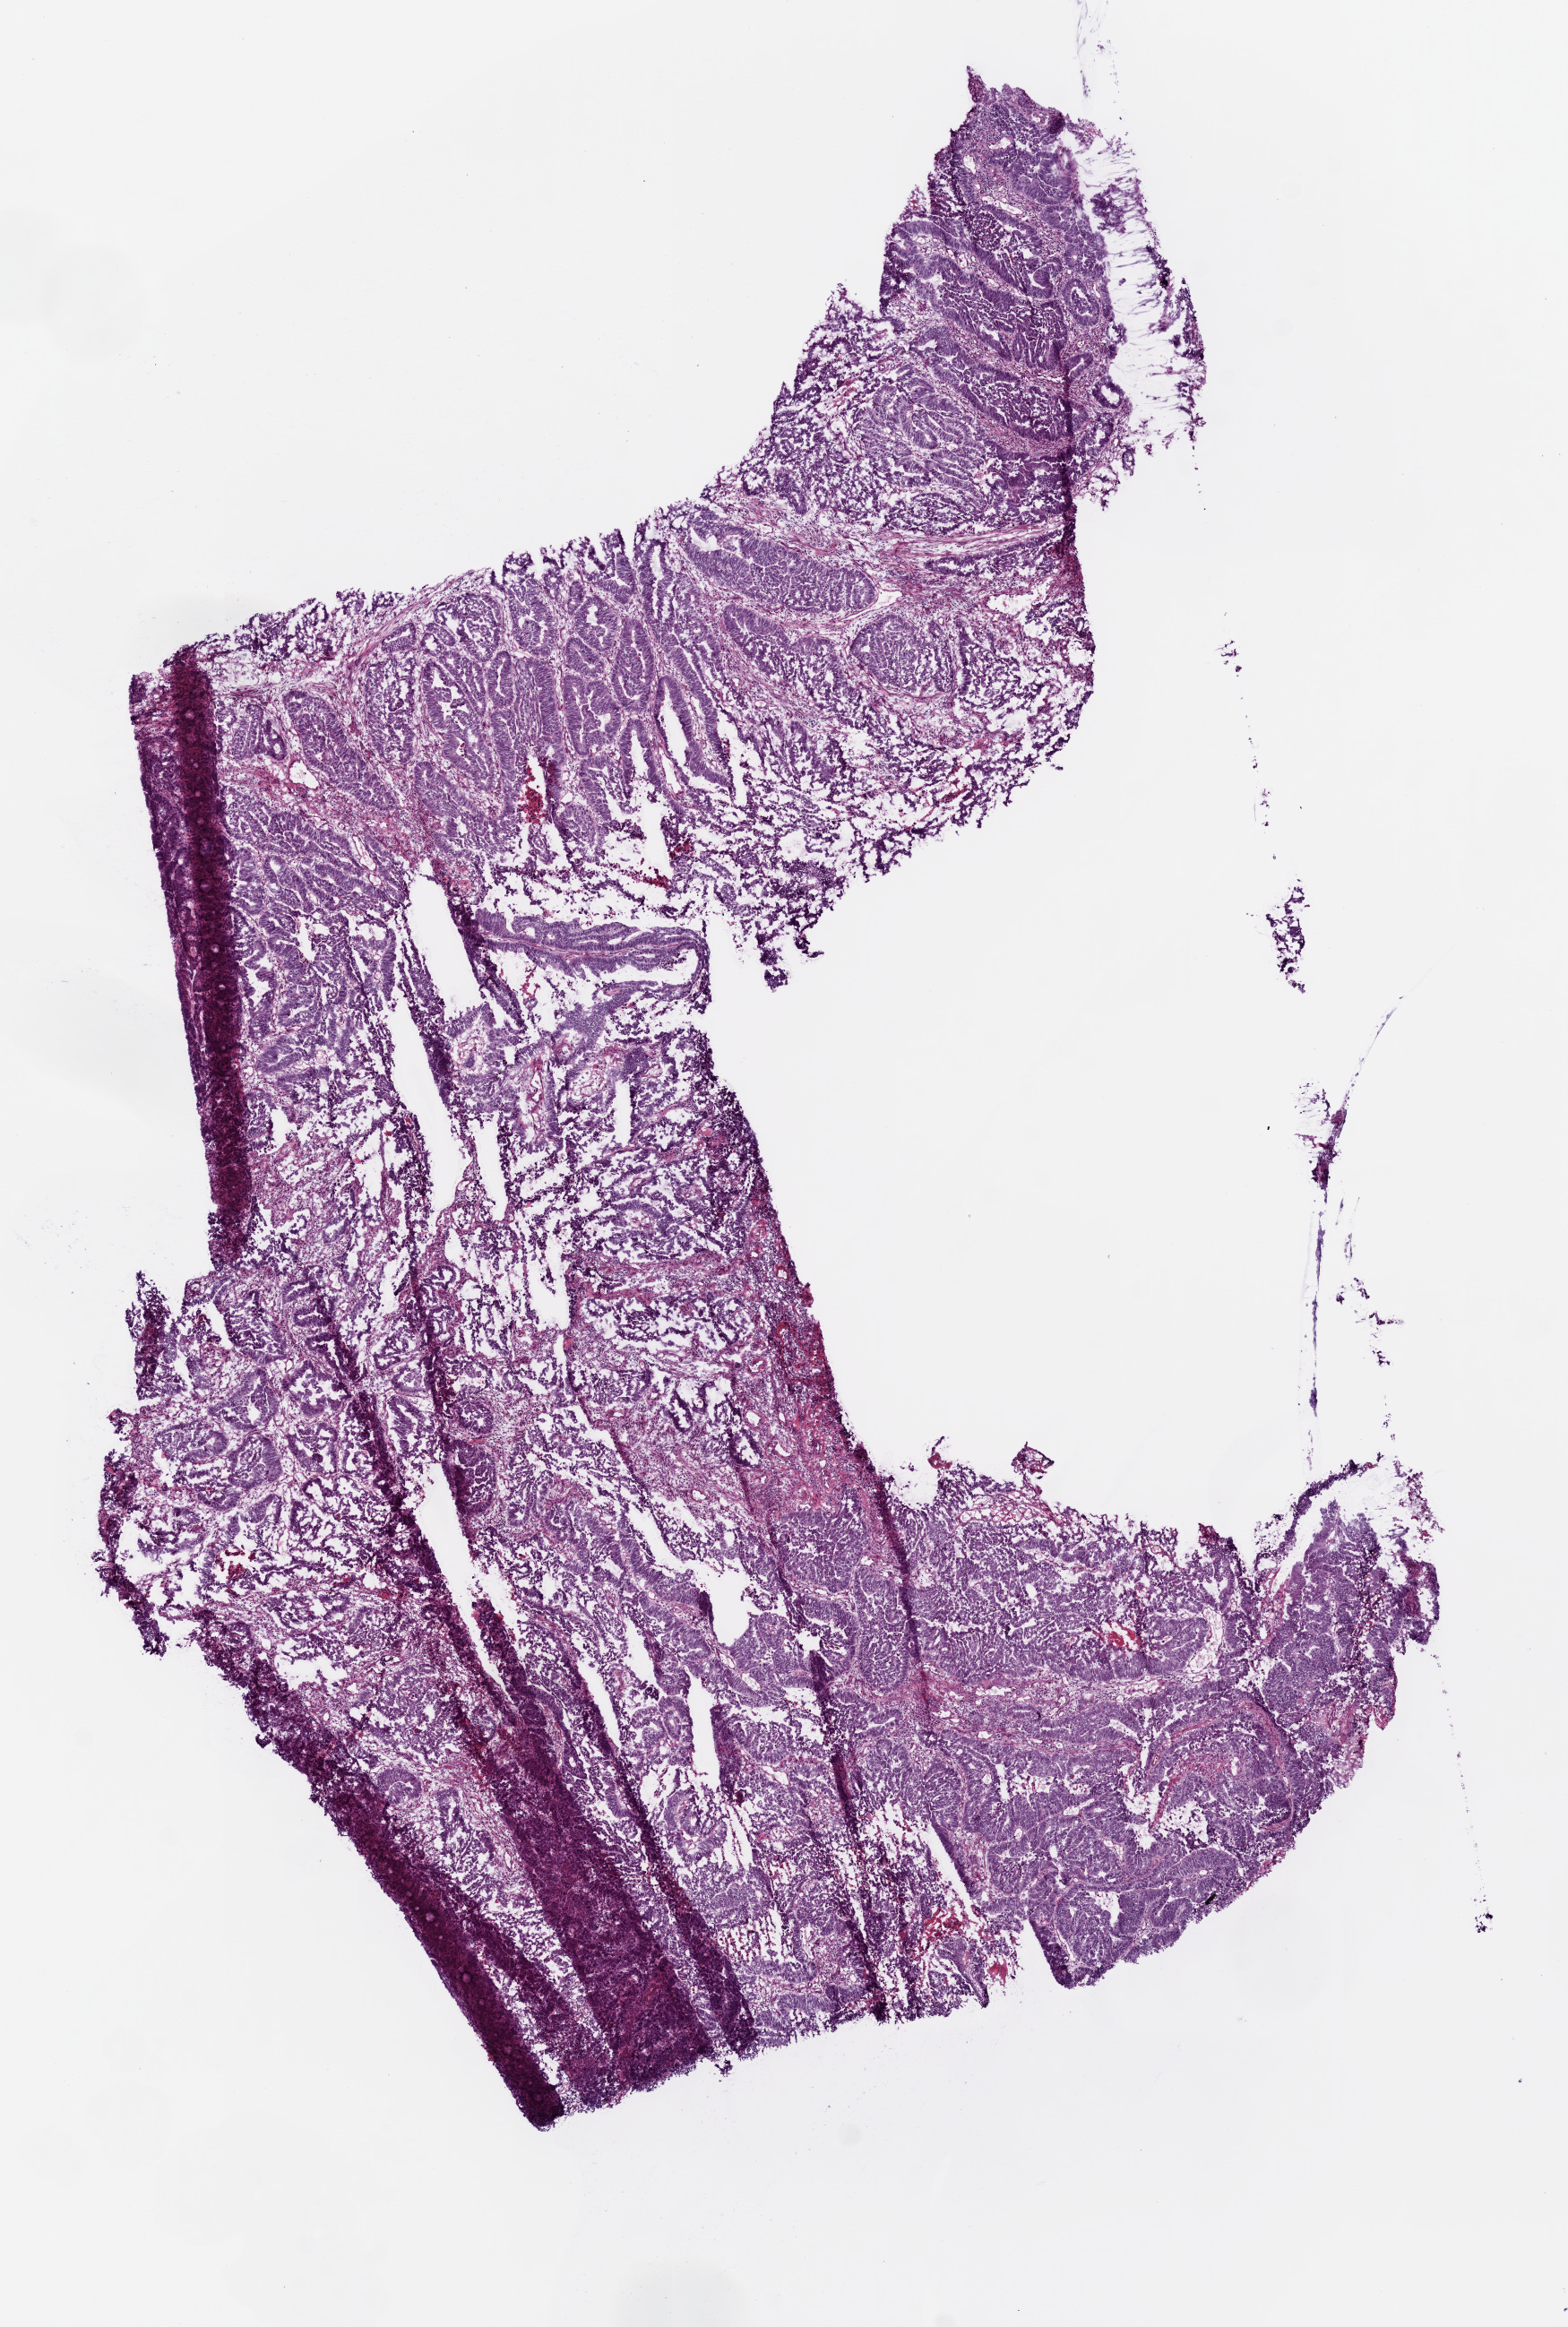
Digitized H&E-stained tissue section (whole slide) — shown as a low-resolution overview of the whole scanned area (about 7.0 x 10.4 mm, from a 20x scan); frozen section from the top of the tissue portion; sample: primary tumour, rectum. Male patient; age at initial diagnosis 65 years. Composition of this section per pathologist review: tumour cells 80%, tumour nuclei 75%, normal cells 0%, stromal cells 5%, necrosis 15%.
- lymph nodes positive (case pathology): 0 of 17 examined
- AJCC pathologic stage: I (6th edition)
- diagnosis: Adenocarcinoma, NOS